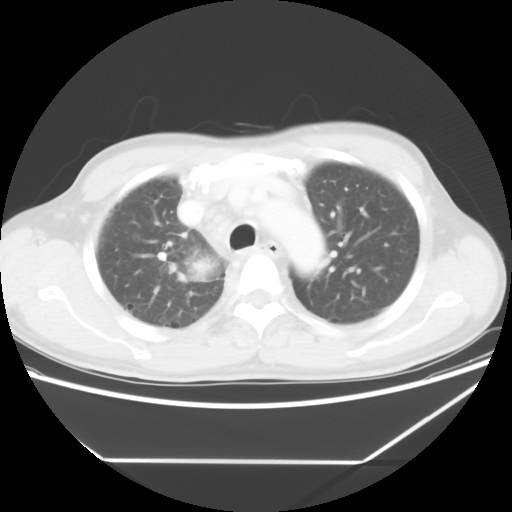
Chest CT, one axial slice; position 46 of 60 along the scan axis; reconstruction kernel STANDARD; lung window (W 1500 / L -600 HU); 5 mm slice thickness; 512 × 512 image matrix, field of view 367 × 367 mm. Male patient, age 58 years. Case-level facts recorded for this patient, not image findings: clinical TNM (as recorded): T2 N2 M0.
Structures marked on this image (rectangle marked by the reading radiologist):
- lung tumour (recorded histology: squamous cell carcinoma): bounding box (x1, y1, x2, y2) in pixels: (188, 258, 211, 280)